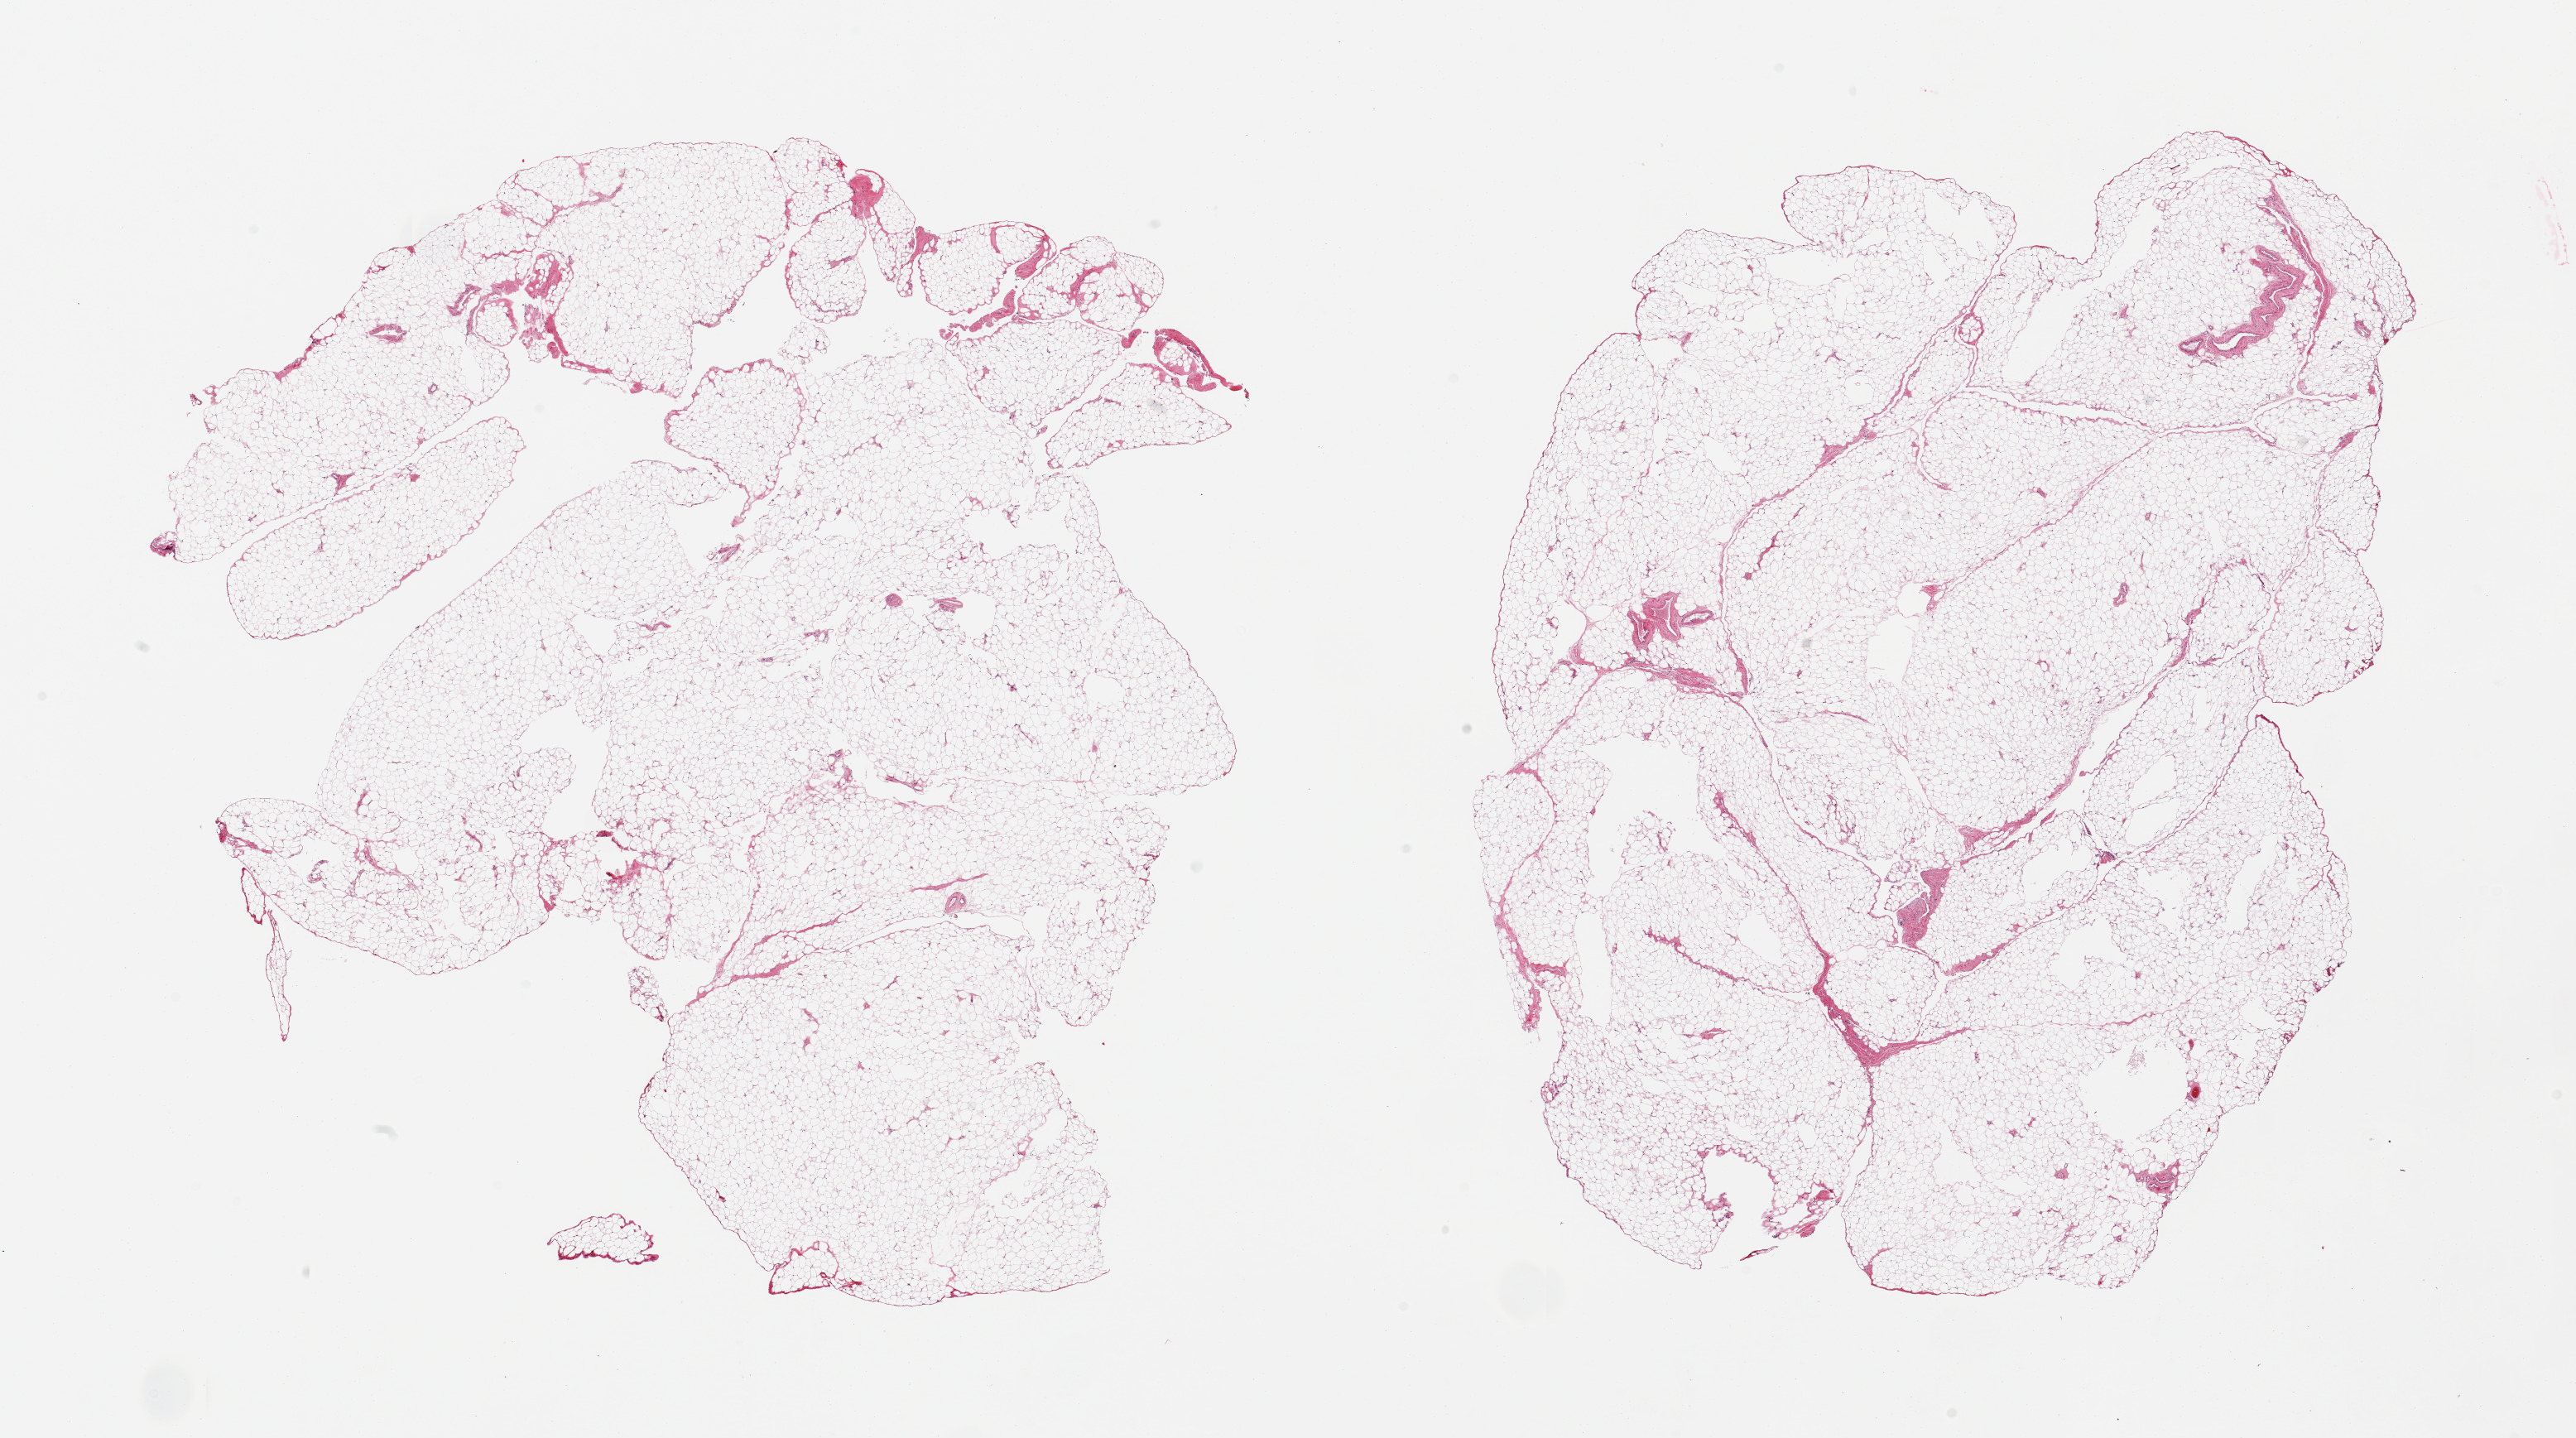
Whole-slide image, haematoxylin and eosin stain — low-resolution overview of the scanned area, about 24.6 x 13.7 mm; PAXgene-fixed, paraffin-embedded tissue; target tissue: omentum; donor tissue sample.
• pathologist's review note for this sample: 2 pieces, minimal interstitial fascia/vascular elements